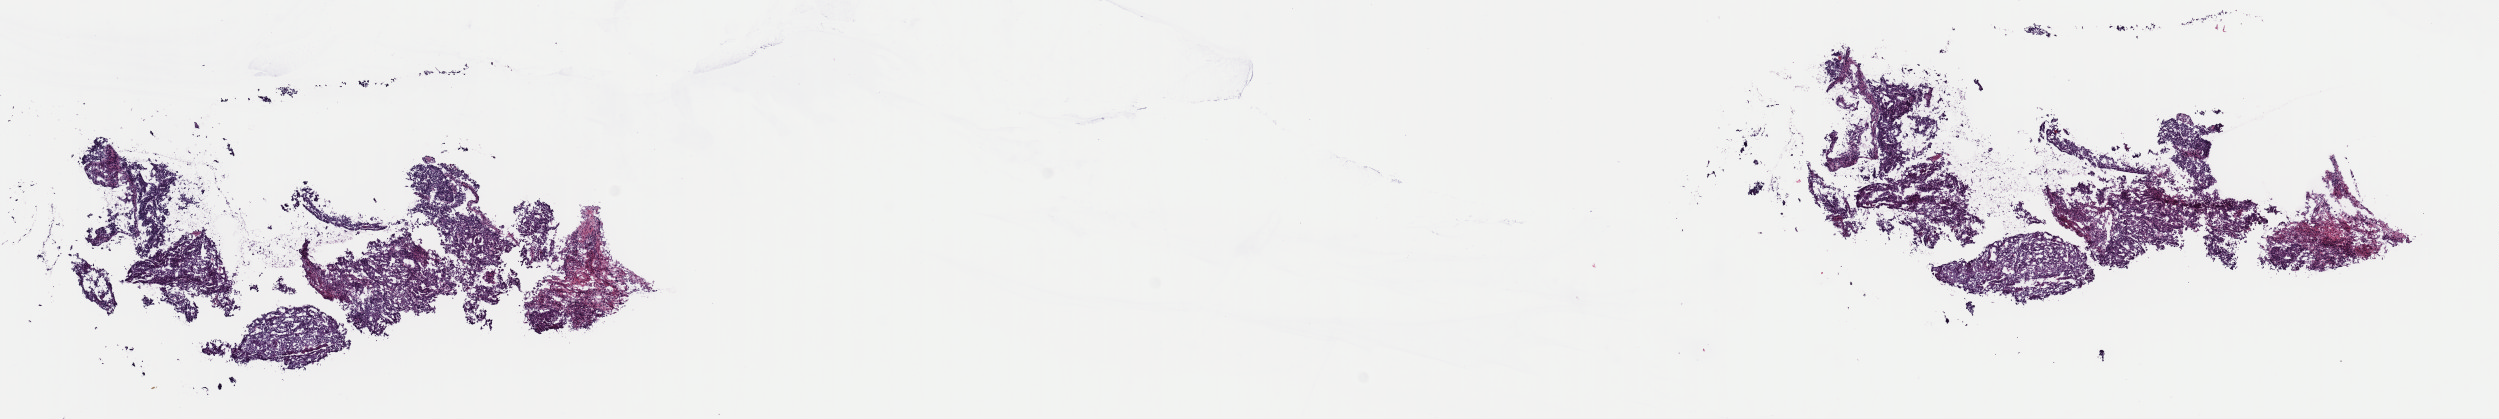
Whole-slide histology image, Hematoxylin and eosin (H&E) stained — shown as a low-resolution overview of the whole scanned area (about 19.7 x 3.3 mm). Frozen section from the top of the tissue portion. Uterus, primary tumour sample. Female, age 57 years at initial diagnosis. Histologic grade: G1 (well differentiated). Slide review estimates, as recorded: tumour cells 80%, tumour nuclei 90%, normal cells 10%, stromal cells 10%, necrosis 0%. Inflammatory infiltration, as recorded: lymphocyte infiltration 0%, monocyte infiltration 0%, neutrophil infiltration 0%.
Pathologic diagnosis: Endometrioid adenocarcinoma, NOS (isthmus uteri). FIGO stage: II.